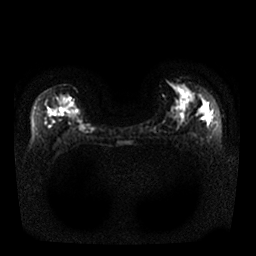
Breast MRI, one axial slice. Slice 16 of 25 in the series (ordered by position). Diffusion-weighted series; image 2 of 4 stored at this slice position (different b-values; order by instance number). 1.5 T. 4 mm slice thickness. 256 × 256 image matrix. Female patient.
Structures marked on this image (manually delineated by an expert):
- tumour on diffusion-weighted imaging: bounding box (x1, y1, x2, y2) in pixels: (55, 106, 70, 116)